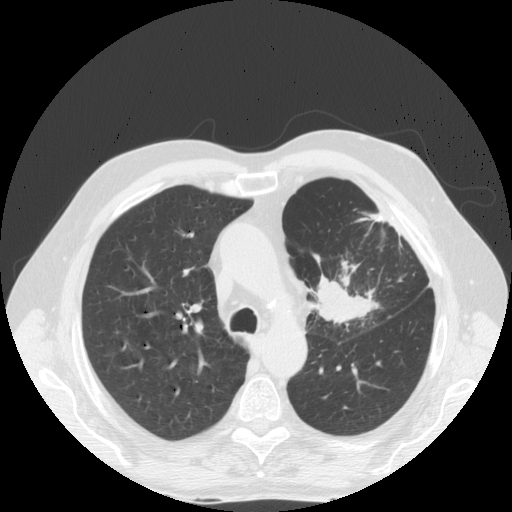
Low-dose screening chest CT, one axial slice. Position 120 of 170 along the scan axis. 140 kVp. Lung window (W 1500 / L -600 HU). 2.5 mm slice thickness. 512 × 512 image matrix, field of view 380 × 380 mm.
Structures marked on this image (manually delineated by an expert):
- lesion 1 (tumor, upper lobe of left lung): box from (x=316, y=275) to (x=380, y=326) px